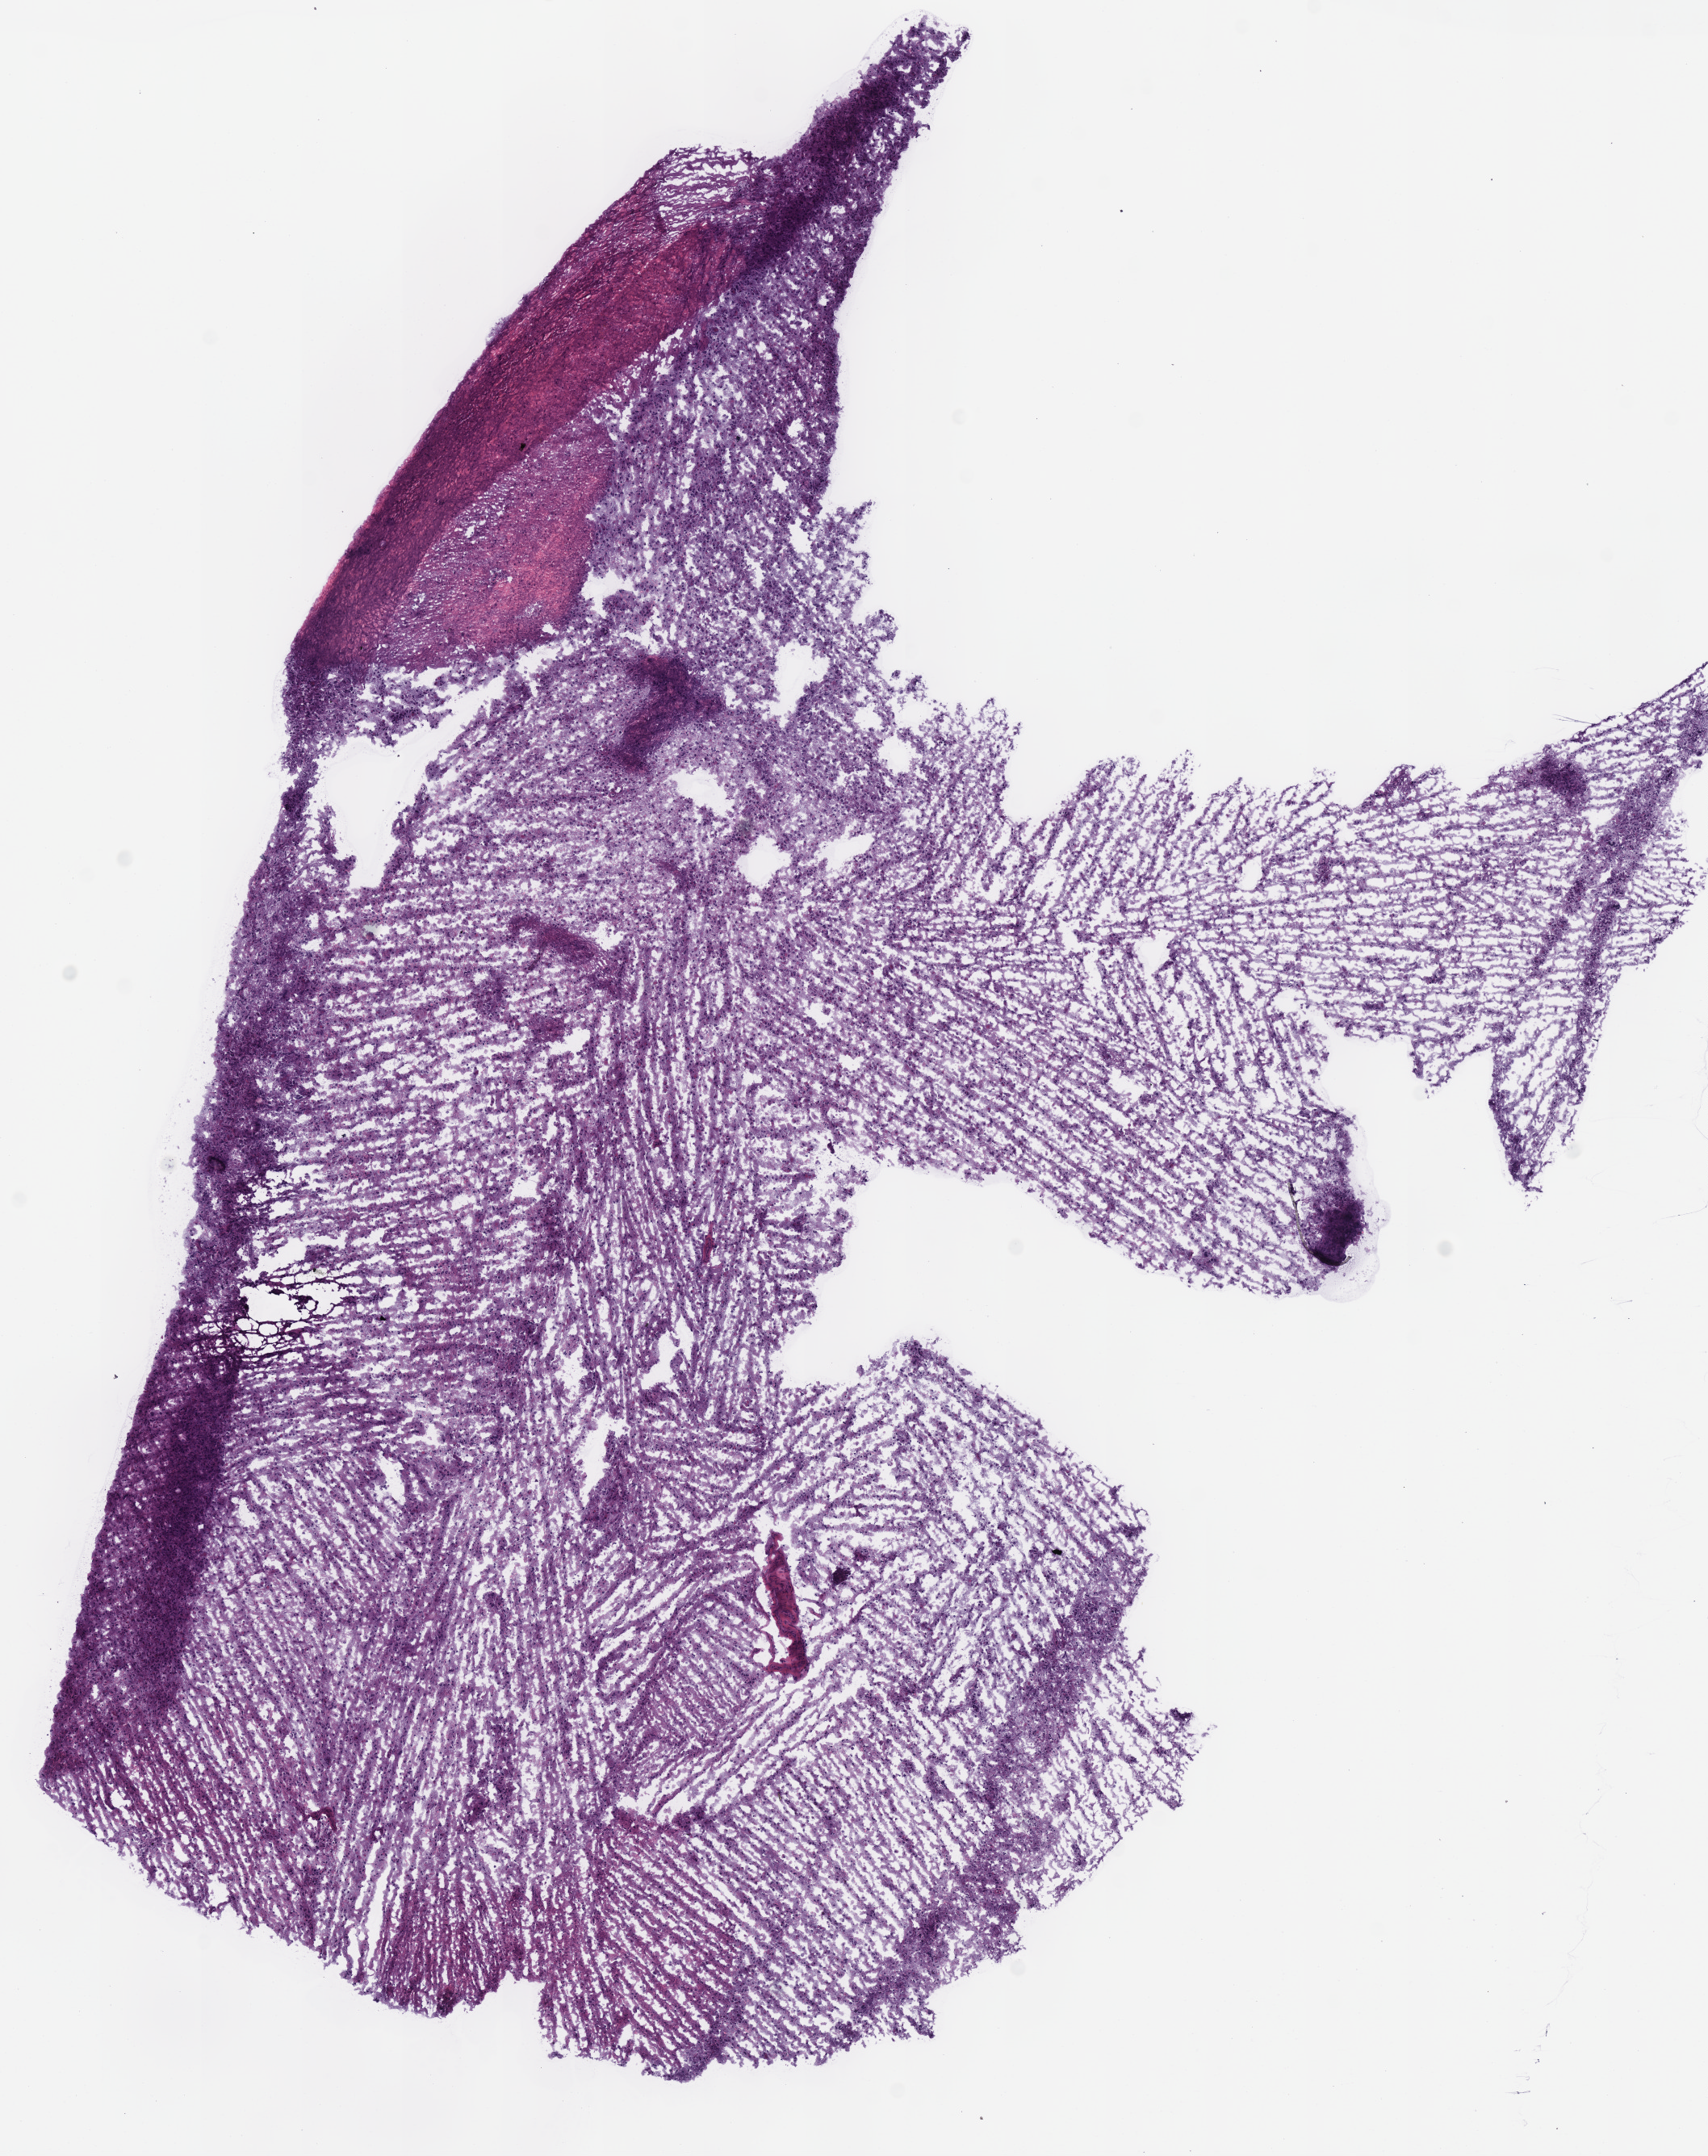
Whole-slide histology image, Hematoxylin and eosin (H&E) stained — whole scanned area (about 8.3 x 10.5 mm) shown as a low-resolution overview. Frozen section from the top of the tissue portion. Sample: primary tumour, brain. Female, age 69 years at initial diagnosis. Histologic grade: G2 (moderately differentiated). Pathologist review of this section (percent, as recorded): tumour cells 100%, tumour nuclei 75%, normal cells 0%, stromal cells 0%, necrosis 0%.
Laterality: right. Histologic diagnosis: Mixed glioma (cerebrum).